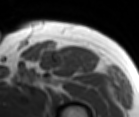
MRI of an extremity soft-tissue mass, one axial slice. Position 81 of 86 along the scan axis. MR volume resampled by the dataset authors to the PET/CT grid (not the native acquisition matrix). 139 × 117 image matrix, field of view 136 × 114 mm. Male patient. From the clinical record (not read from this slice): histological type: extraskeletal osteosarcoma; grade: high; site of the primary tumour: thigh.
Structures marked on this image (expert contour drawn on MRI and transferred to this co-registered scan by the dataset authors):
- gross tumour volume (mass): bounding box [x1, y1, x2, y2] px = [95, 55, 101, 65]